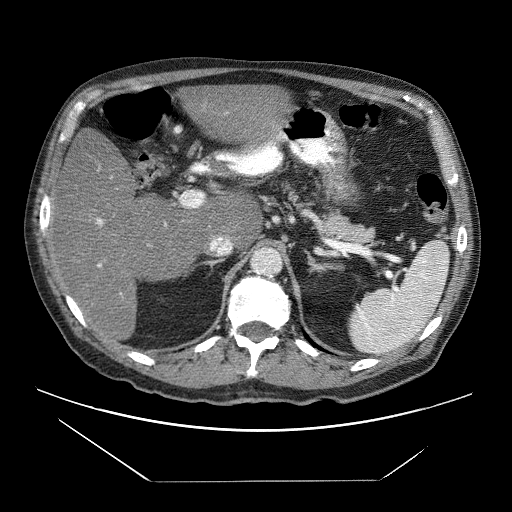
Contrast-enhanced abdominal CT (liver protocol), one axial slice; slice 36 of 83 in the series (ordered by position); 120 kVp; soft-tissue window (W 400 / L 40 HU); 512 × 512 image matrix, field of view 420 × 420 mm. Case-level facts recorded for this patient, not image findings: diagnosis: hepatocellular carcinoma (patient treated with transarterial chemoembolisation; whether this scan precedes or follows treatment is not stated here); TNM stage (as recorded): Stage-IVB; Child-Pugh class: B.
Annotated regions visible in this slice (semi-automatic segmentation, software-assisted and operator-edited):
- liver parenchyma outside the tumour (the mass and vessels are separate outlines, so this box may not span the whole liver): bounding box <48,83,290,342> (left, top, right, bottom; pixels)
- liver vessels: <96,218,167,267>